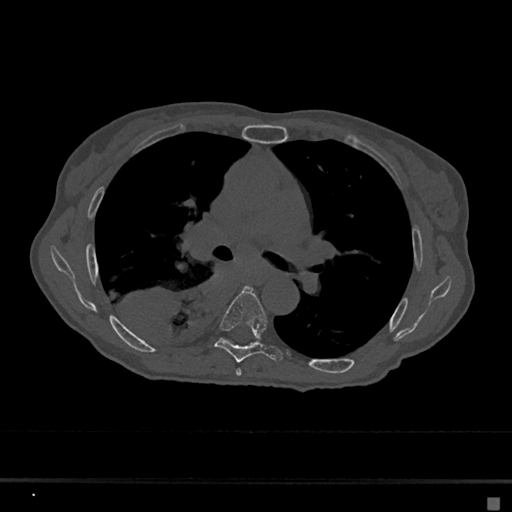
CT including the spine, one axial slice; reconstruction kernel Br40s/3; 120 kVp; bone window (W 1800 / L 400 HU); 0.5 mm slice thickness; 512 × 512 image matrix, field of view 360 × 360 mm. Patient: female, 68 years. From the clinical record (not read from this slice): primary cancer: renal.
Annotated regions visible in this slice (semi-automatically segmented with operator editing):
- T5 vertebra: box from (x=236, y=369) to (x=242, y=376) px
- T6 vertebra: (x=215, y=287)–(x=283, y=363)